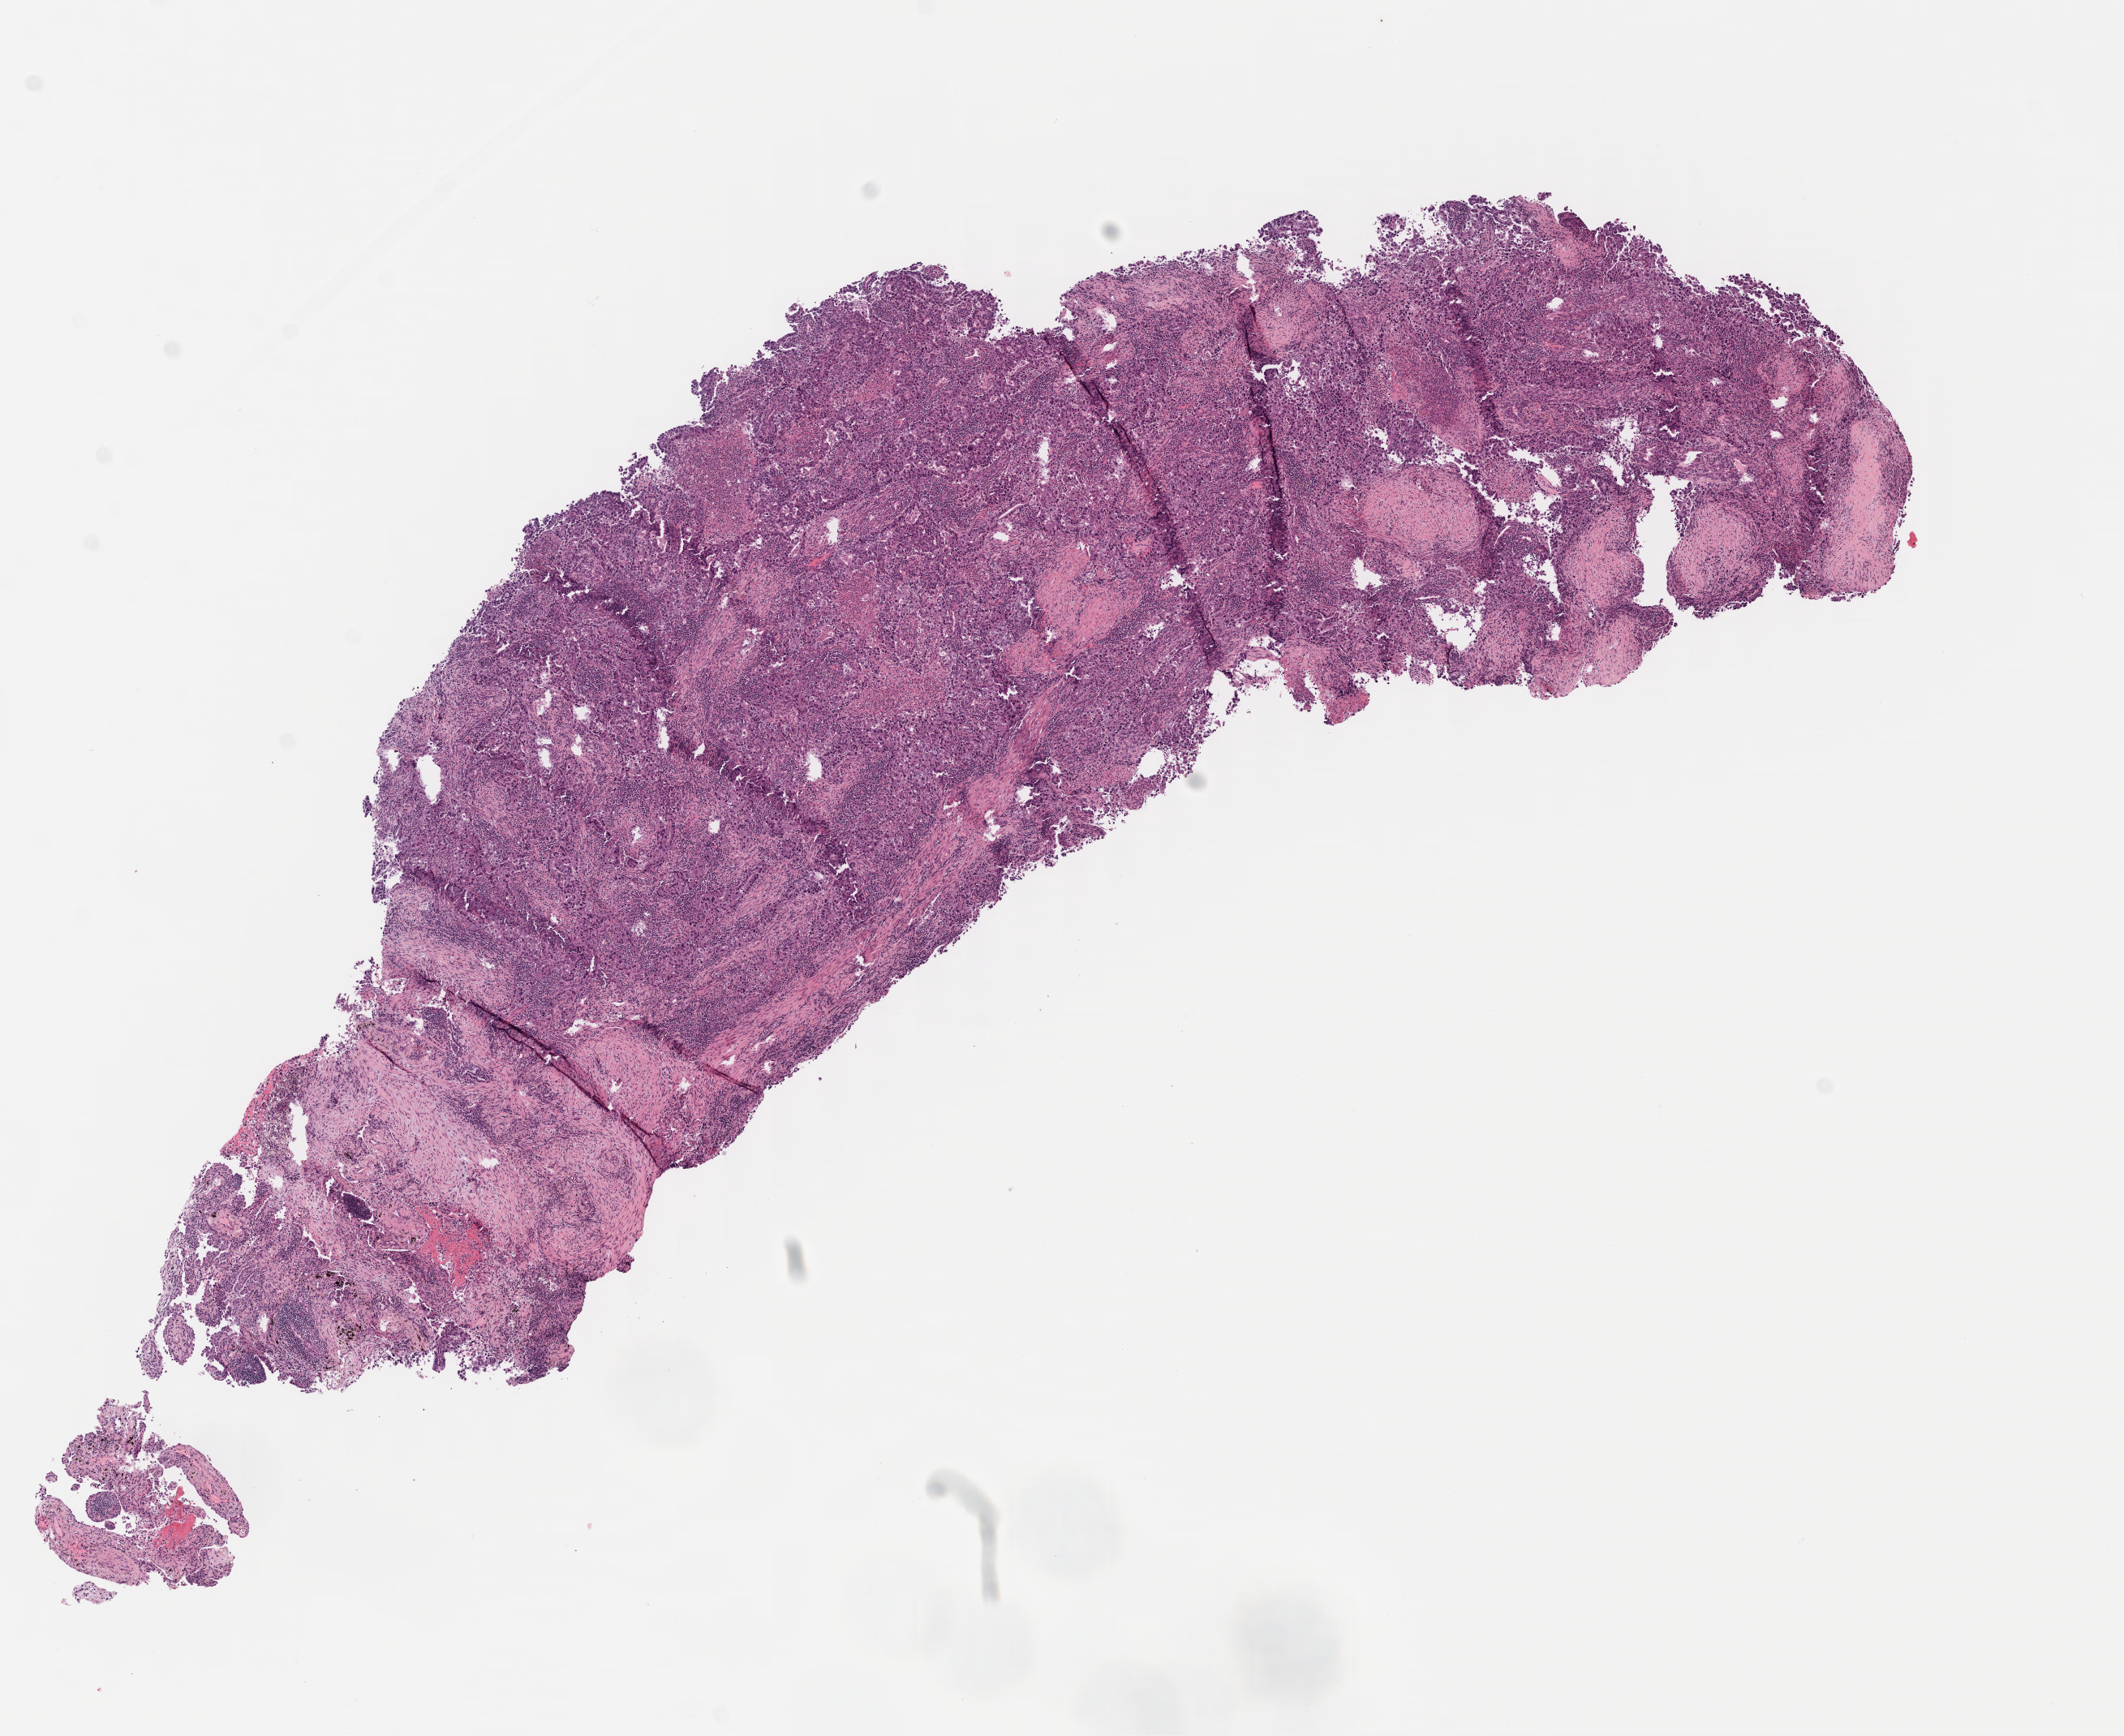
Digitized H&E tissue section (whole slide), a low-resolution overview of the entire scanned area, about 10.3 x 8.4 mm, formalin-fixed paraffin-embedded (FFPE) diagnostic section, lung, primary tumour sample. Male, age 59 years at initial diagnosis.
• diagnosis: Adenocarcinoma, NOS (upper lobe, lung)
• laterality: right
• AJCC pathologic stage: IIA (7th edition)